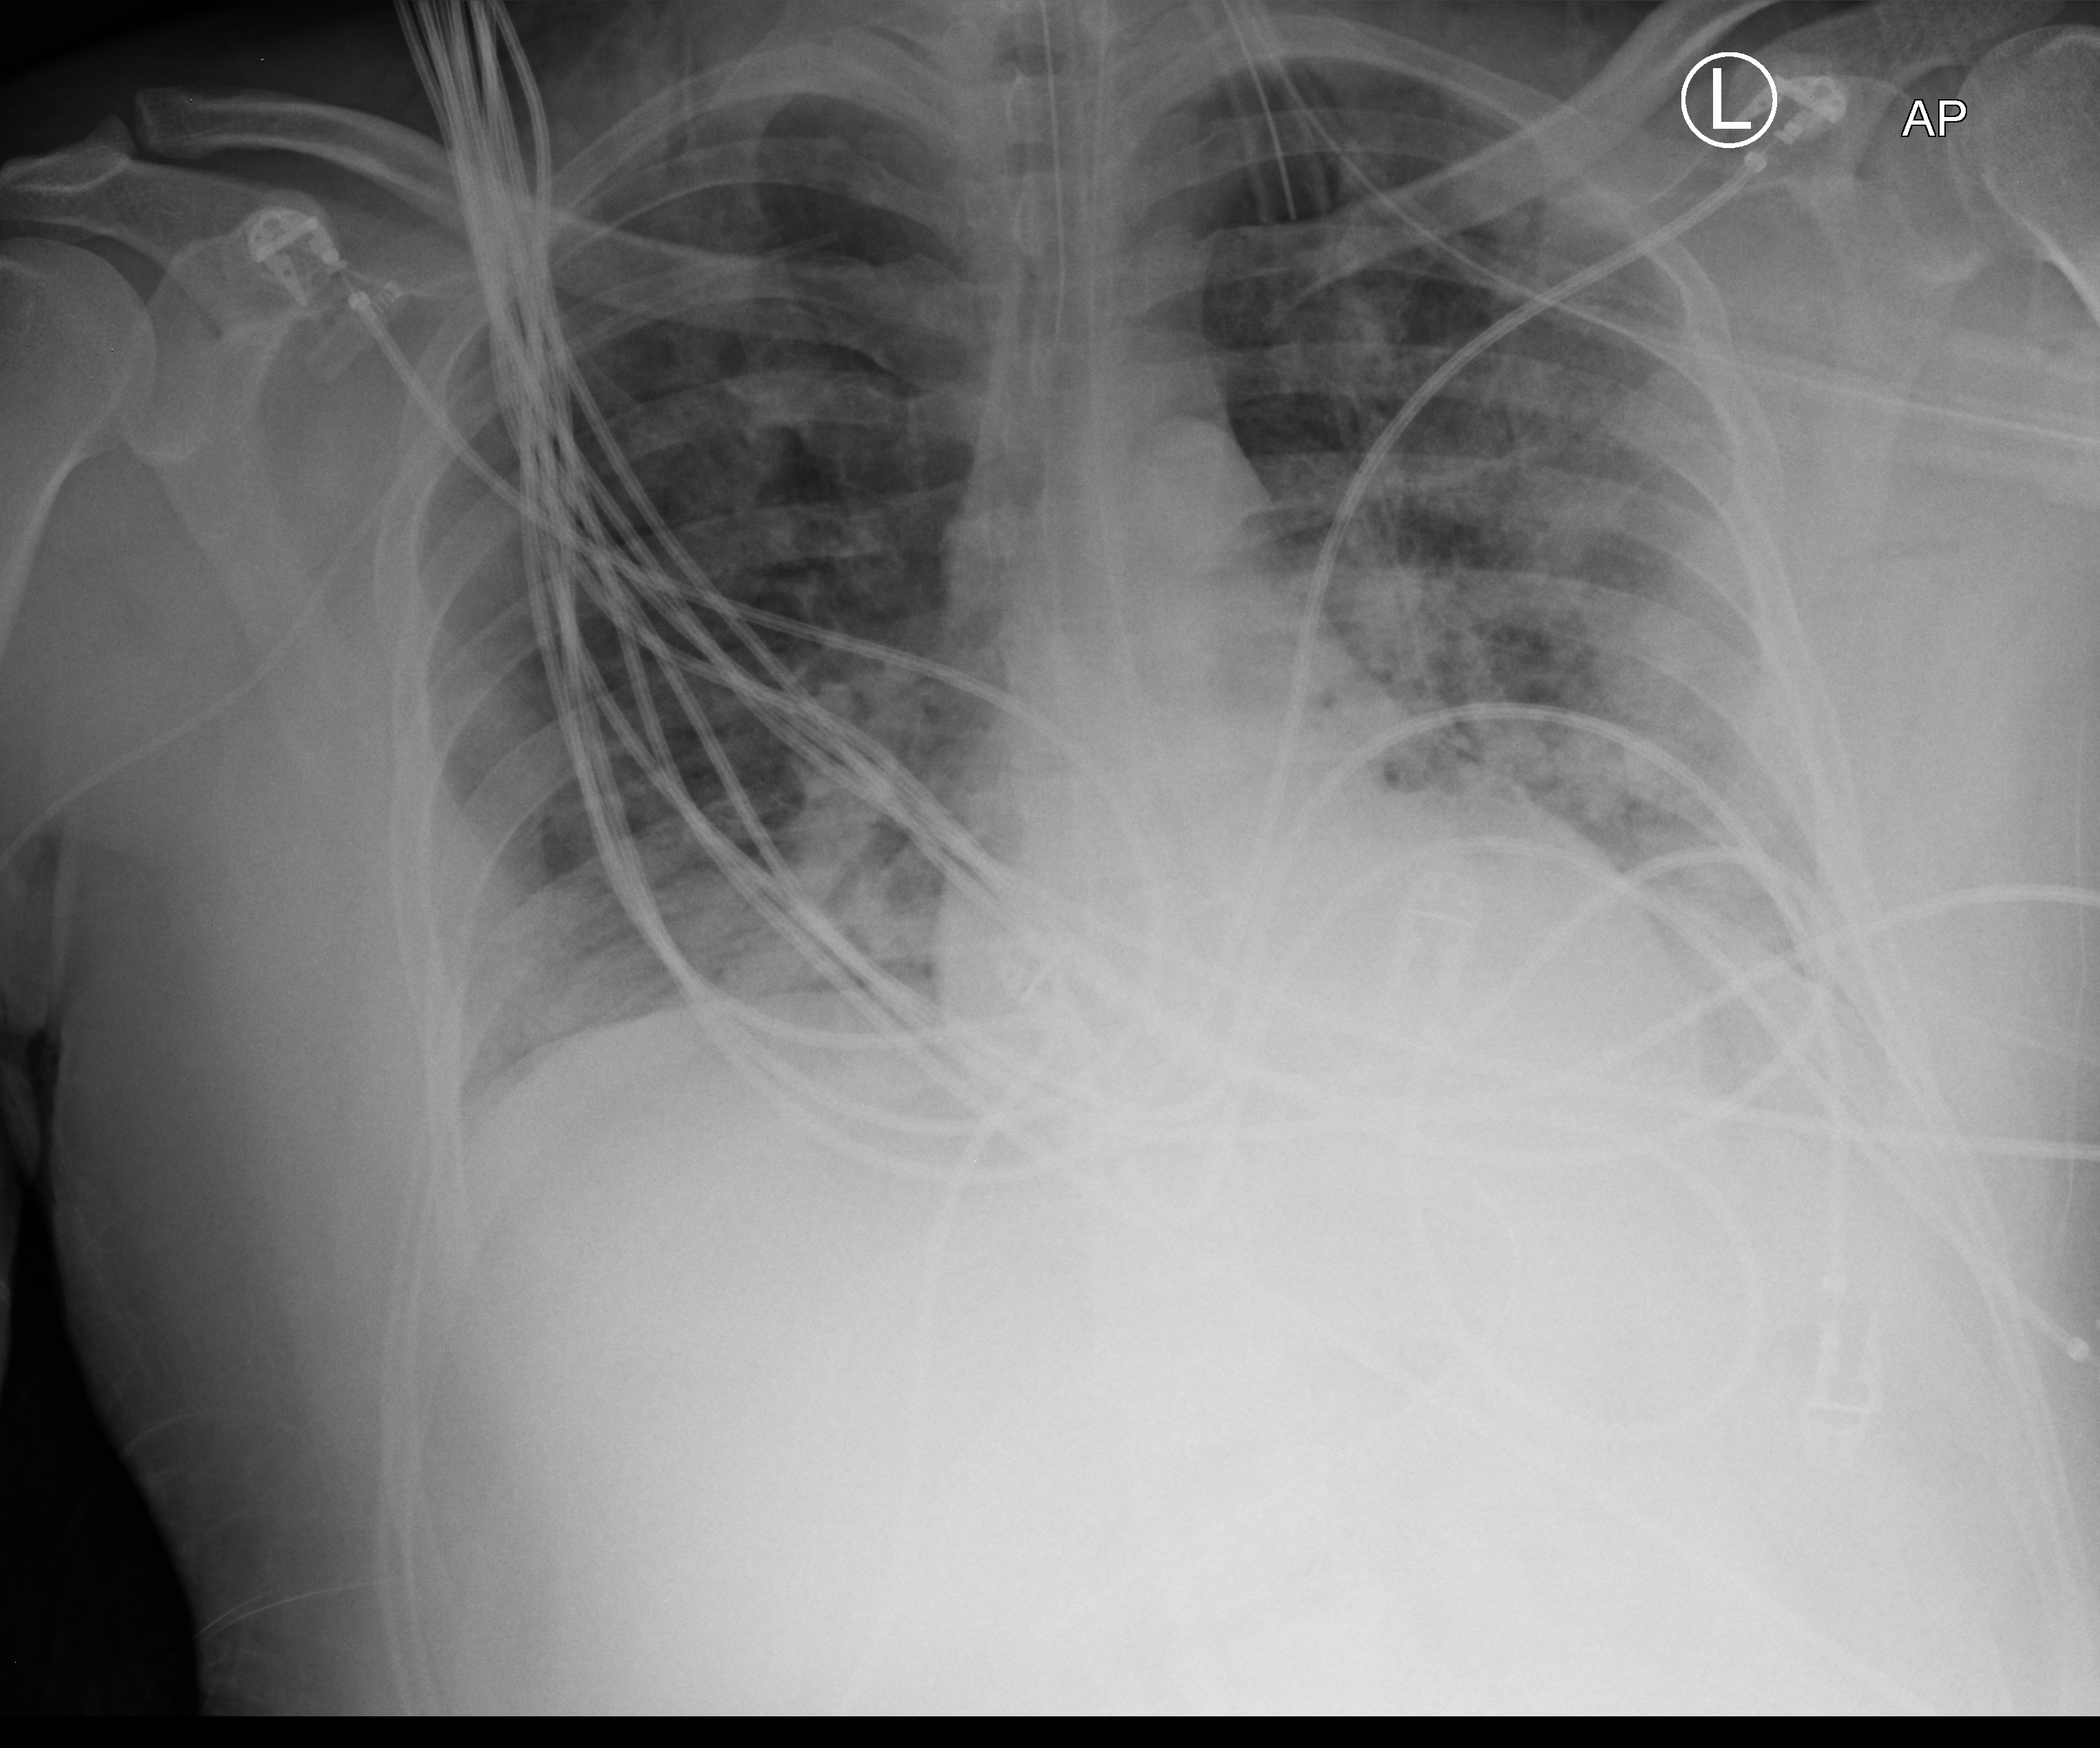
Chest X-ray (portable); anteroposterior (AP) projection. Male patient hospitalised with COVID-19, age 18–59 years.
Admission-level facts for this patient (not findings on this image; timing relative to this image not recorded):
- mechanically ventilated during this hospital stay: yes
- hypertension (admission record): no